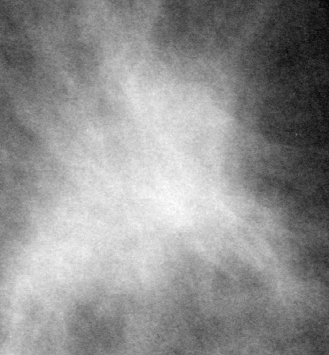
Region of interest cut from a scanned film mammogram (one marked finding), left breast, MLO view.
- Marked abnormality: mass, shape irregular / architectural distortion, margins spiculated; BI-RADS assessment category 4; pathology result (as recorded, not read from the image): malignant.